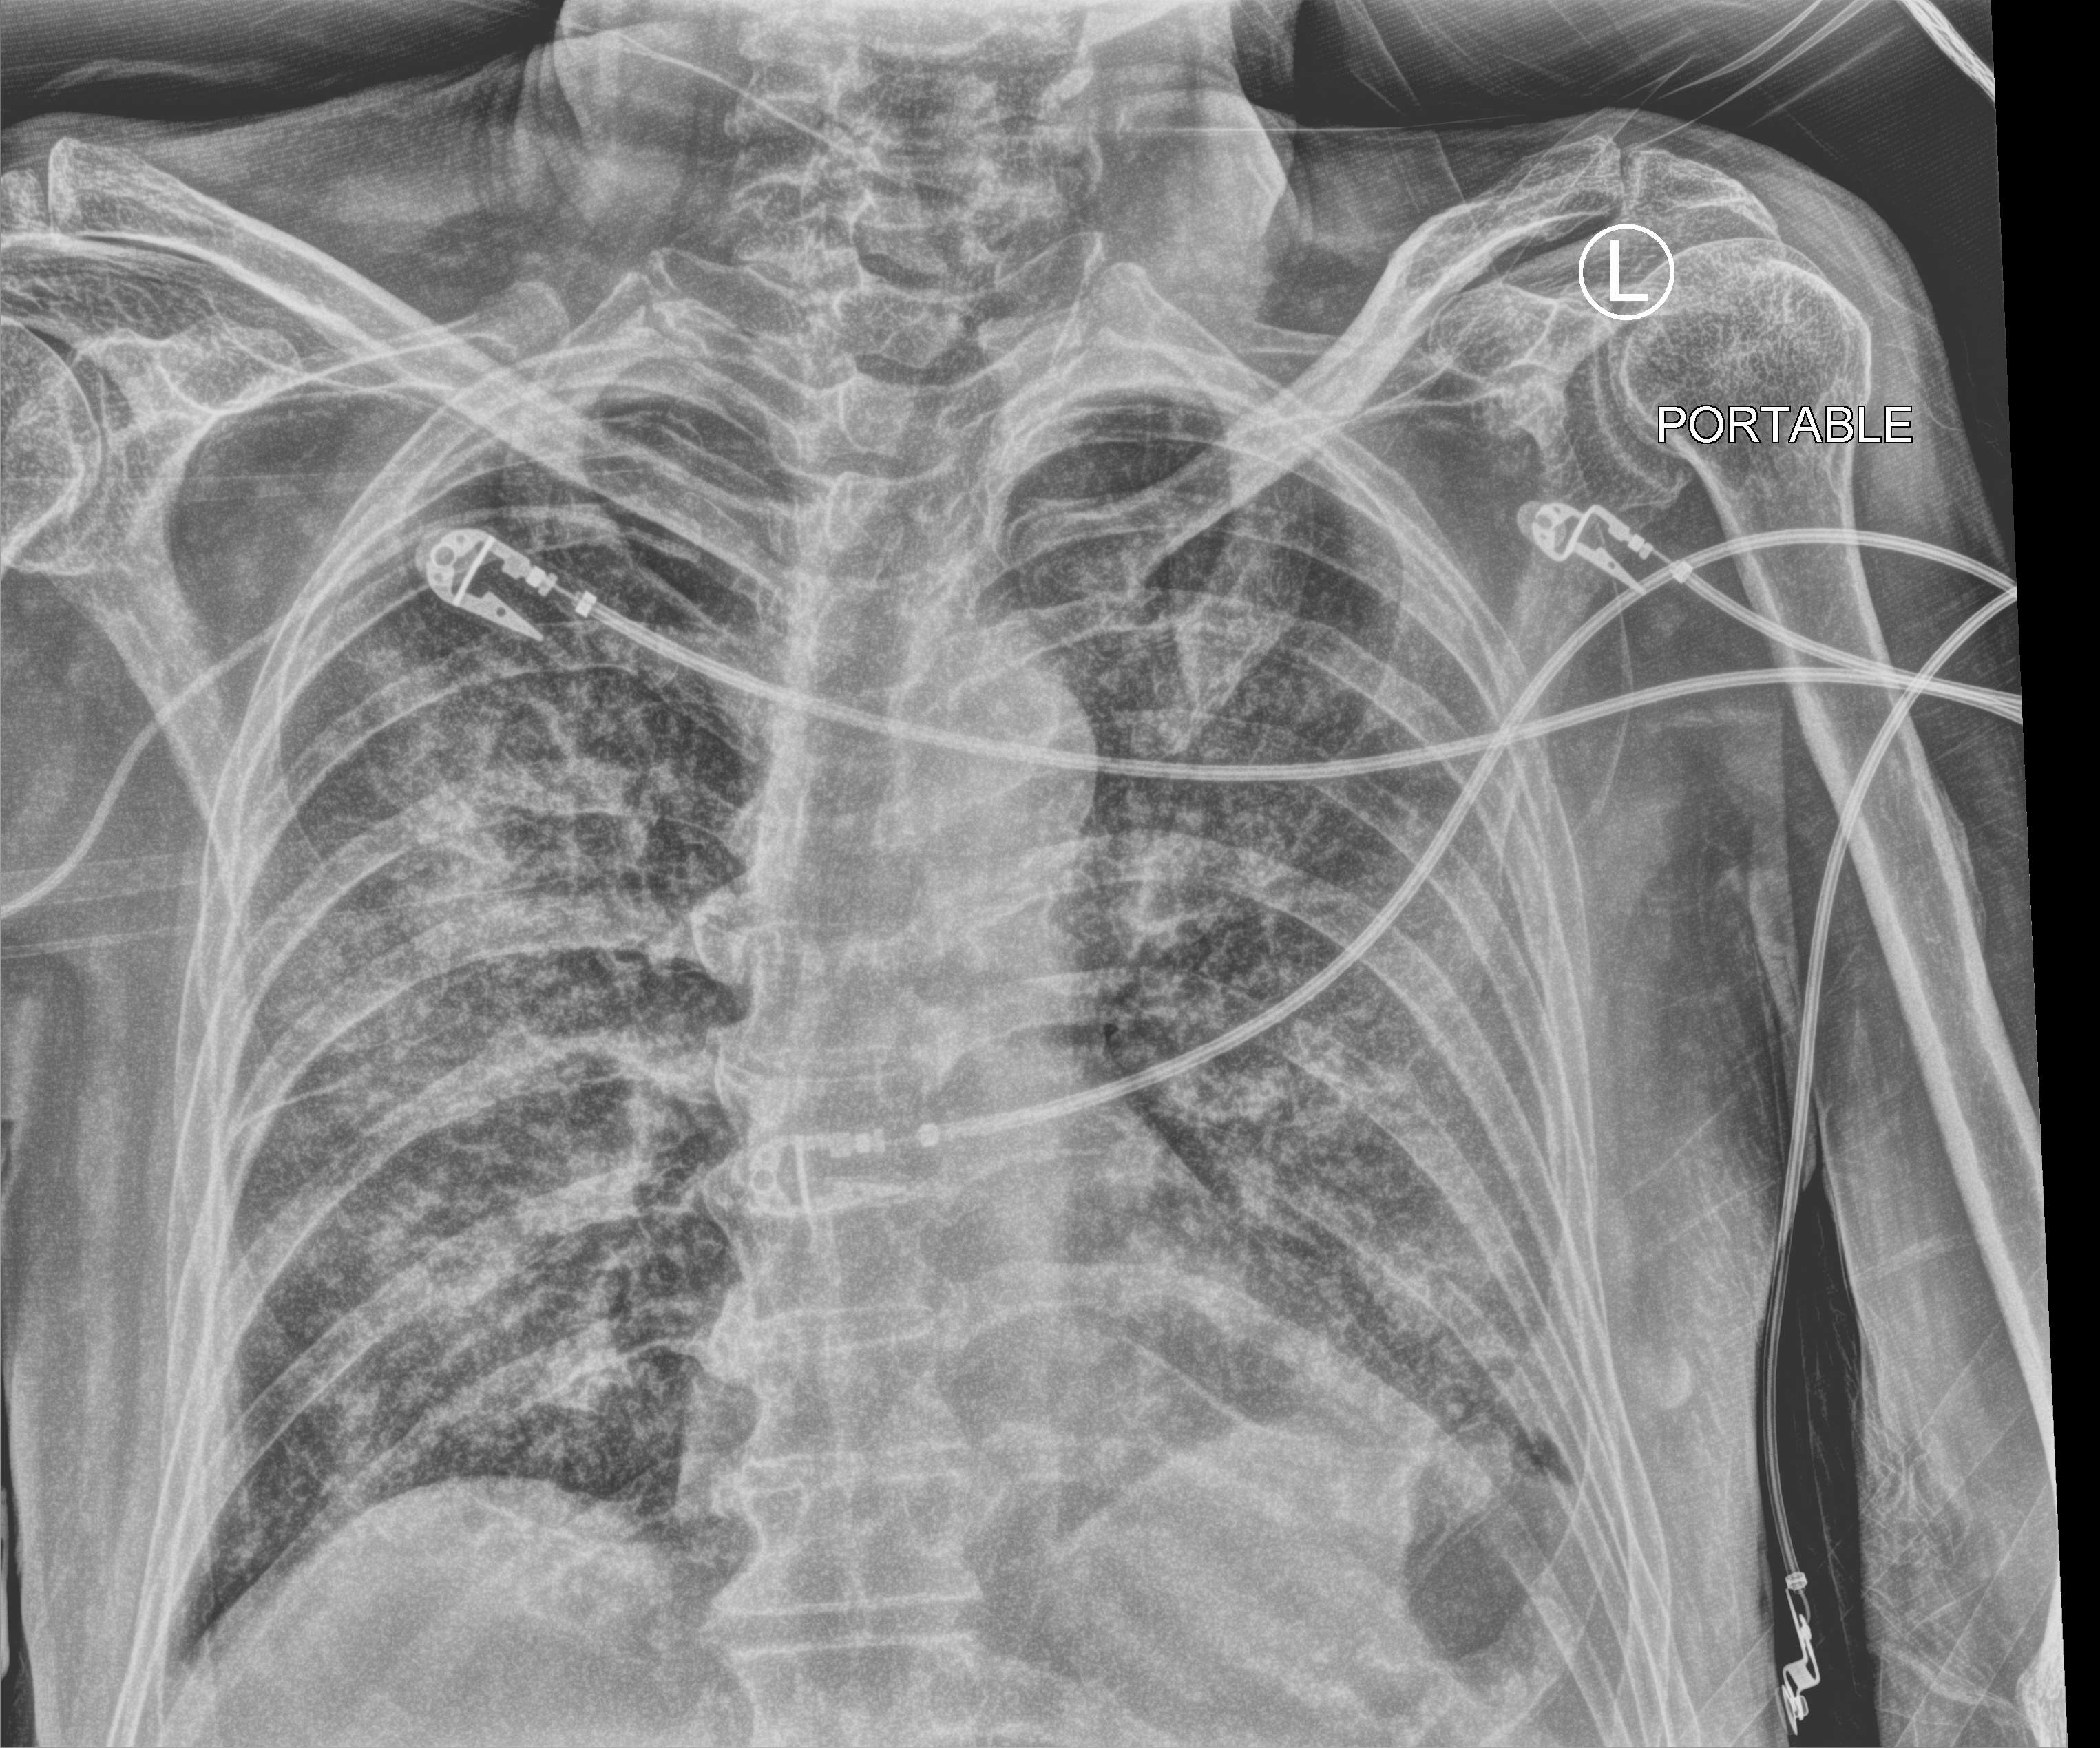
Portable chest radiograph; anteroposterior (AP) projection. Male patient hospitalised with COVID-19, age 60–74 years.
Admission-level facts for this patient (not findings on this image; timing relative to this image not recorded): mechanically ventilated during this hospital stay: yes; other chronic lung disease (admission record): no; admitted to intensive care during this hospital stay: yes.